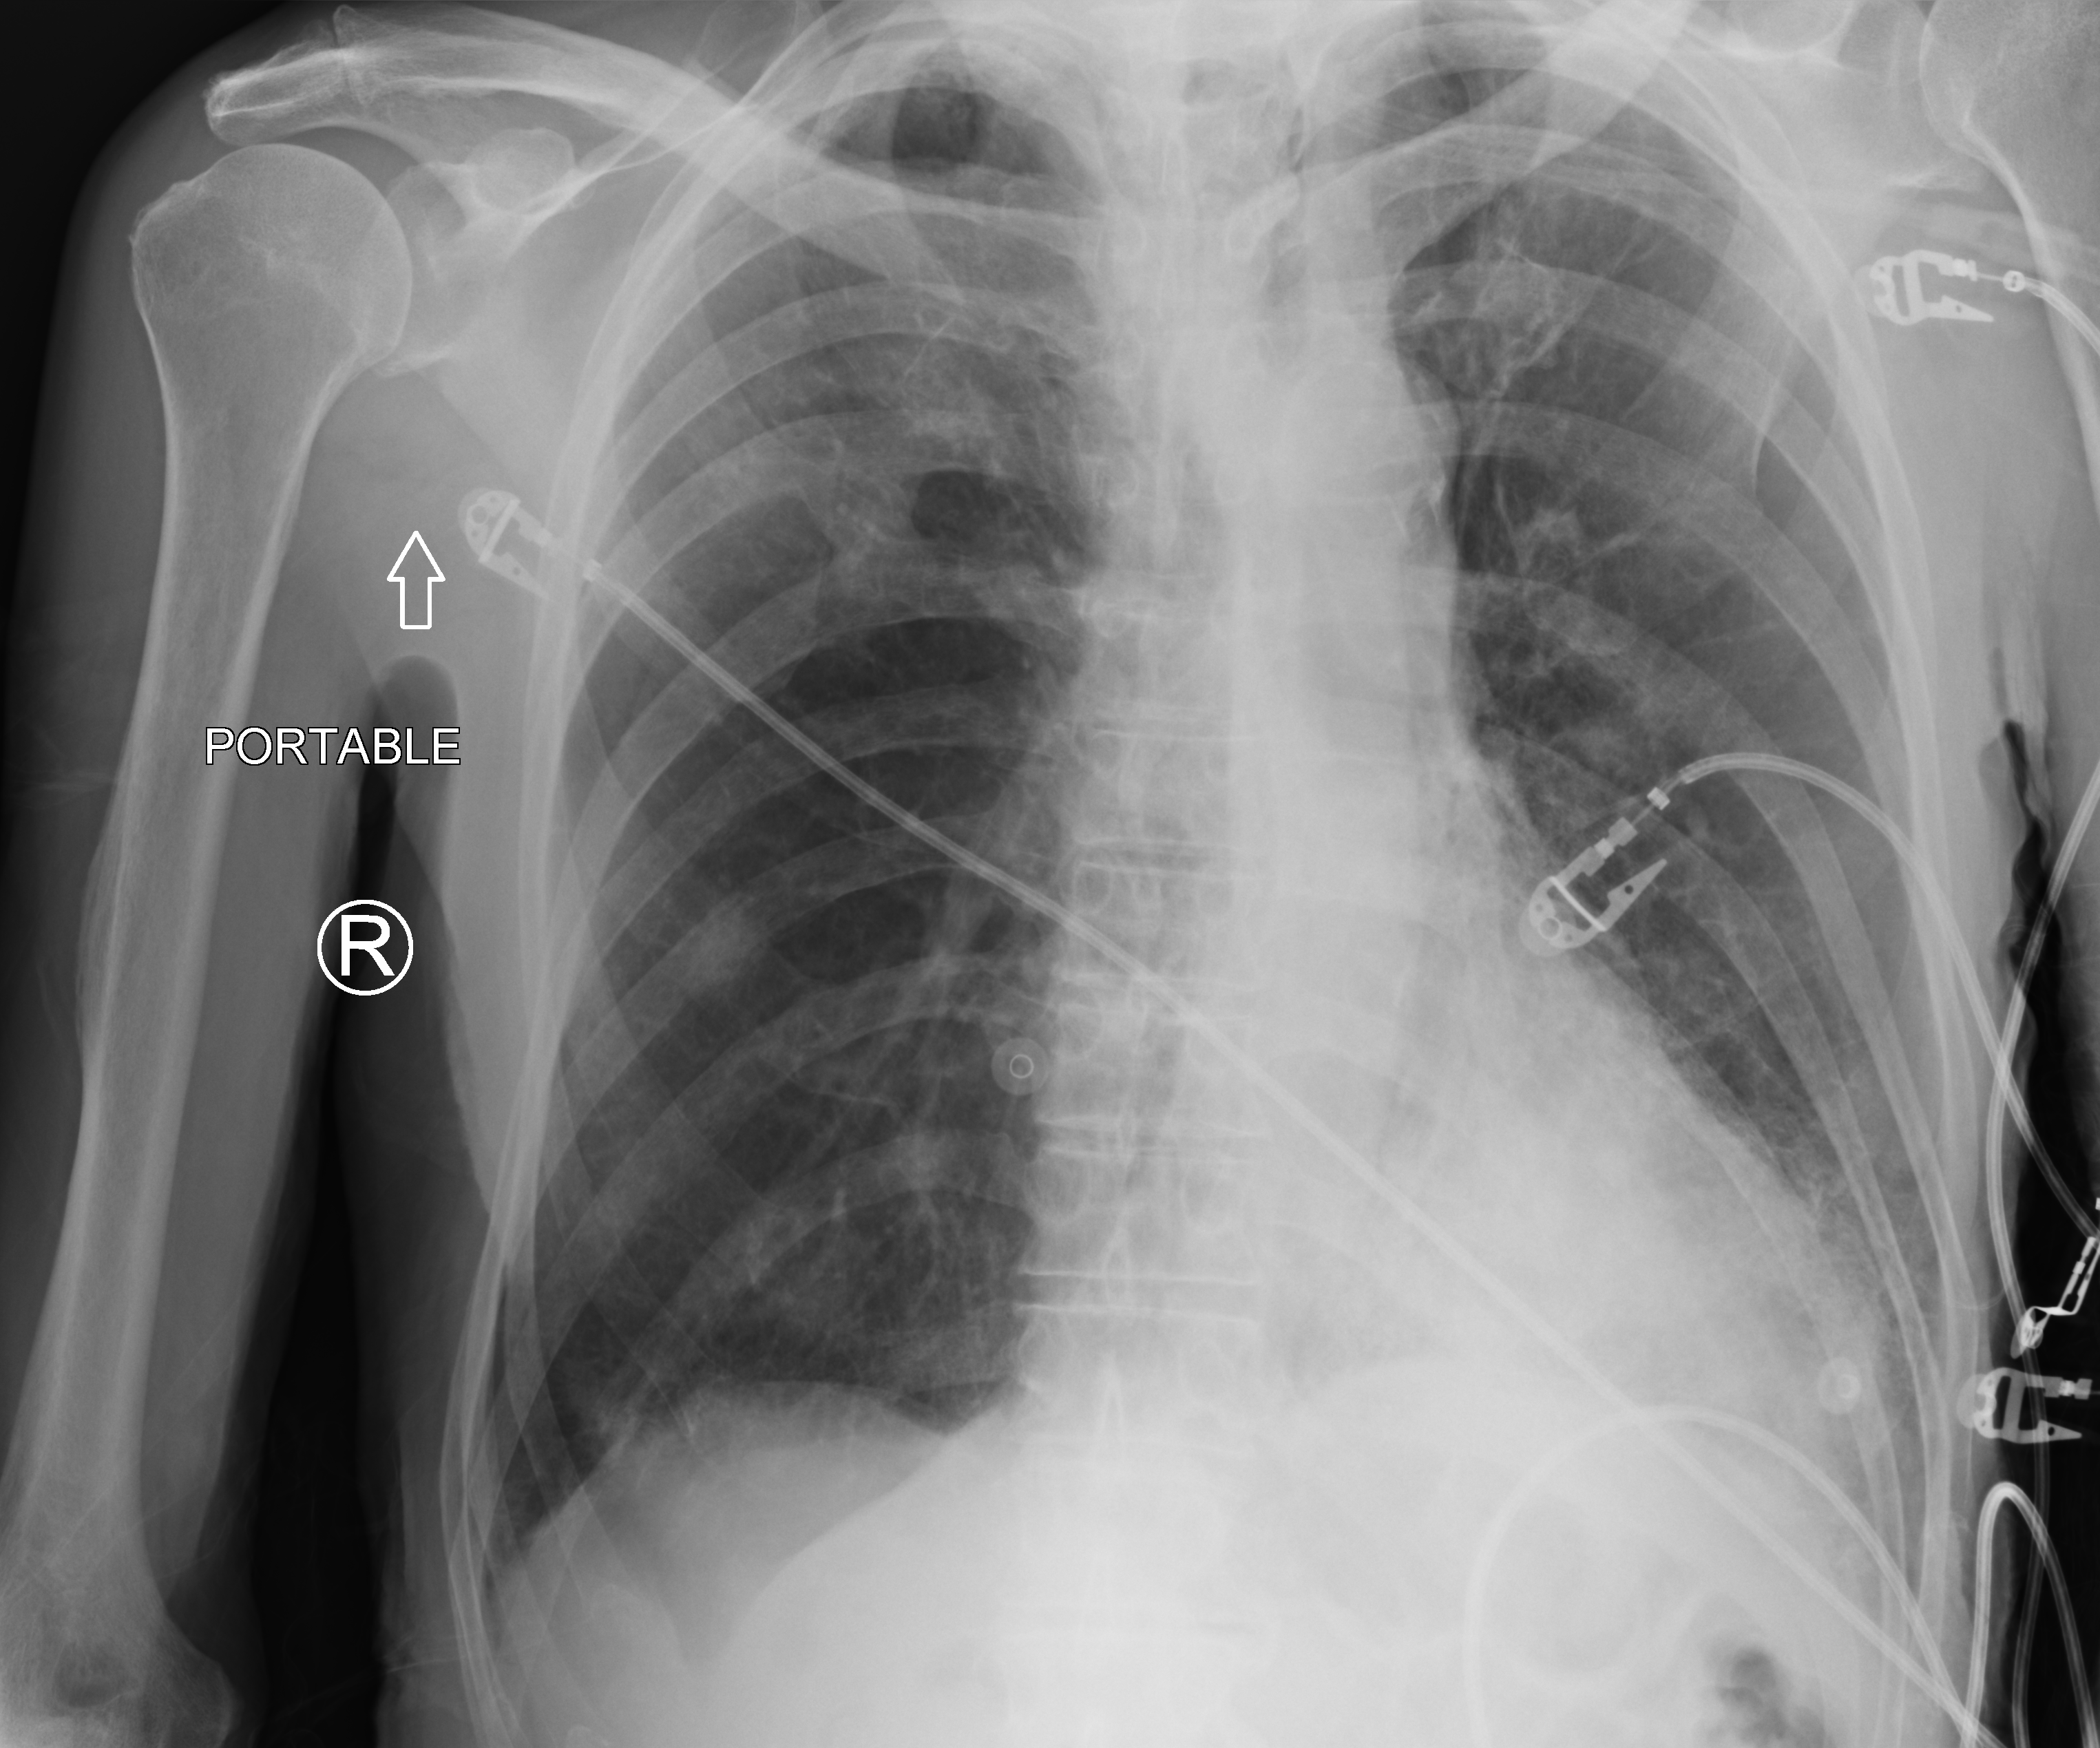
Bedside chest radiograph (computed radiography), anteroposterior (AP) projection. Patient hospitalised with COVID-19; male, aged 75–90 years.
From the hospital-stay record, not from the radiograph (when in the stay this image was taken is not recorded): admitted to intensive care during this hospital stay: no.